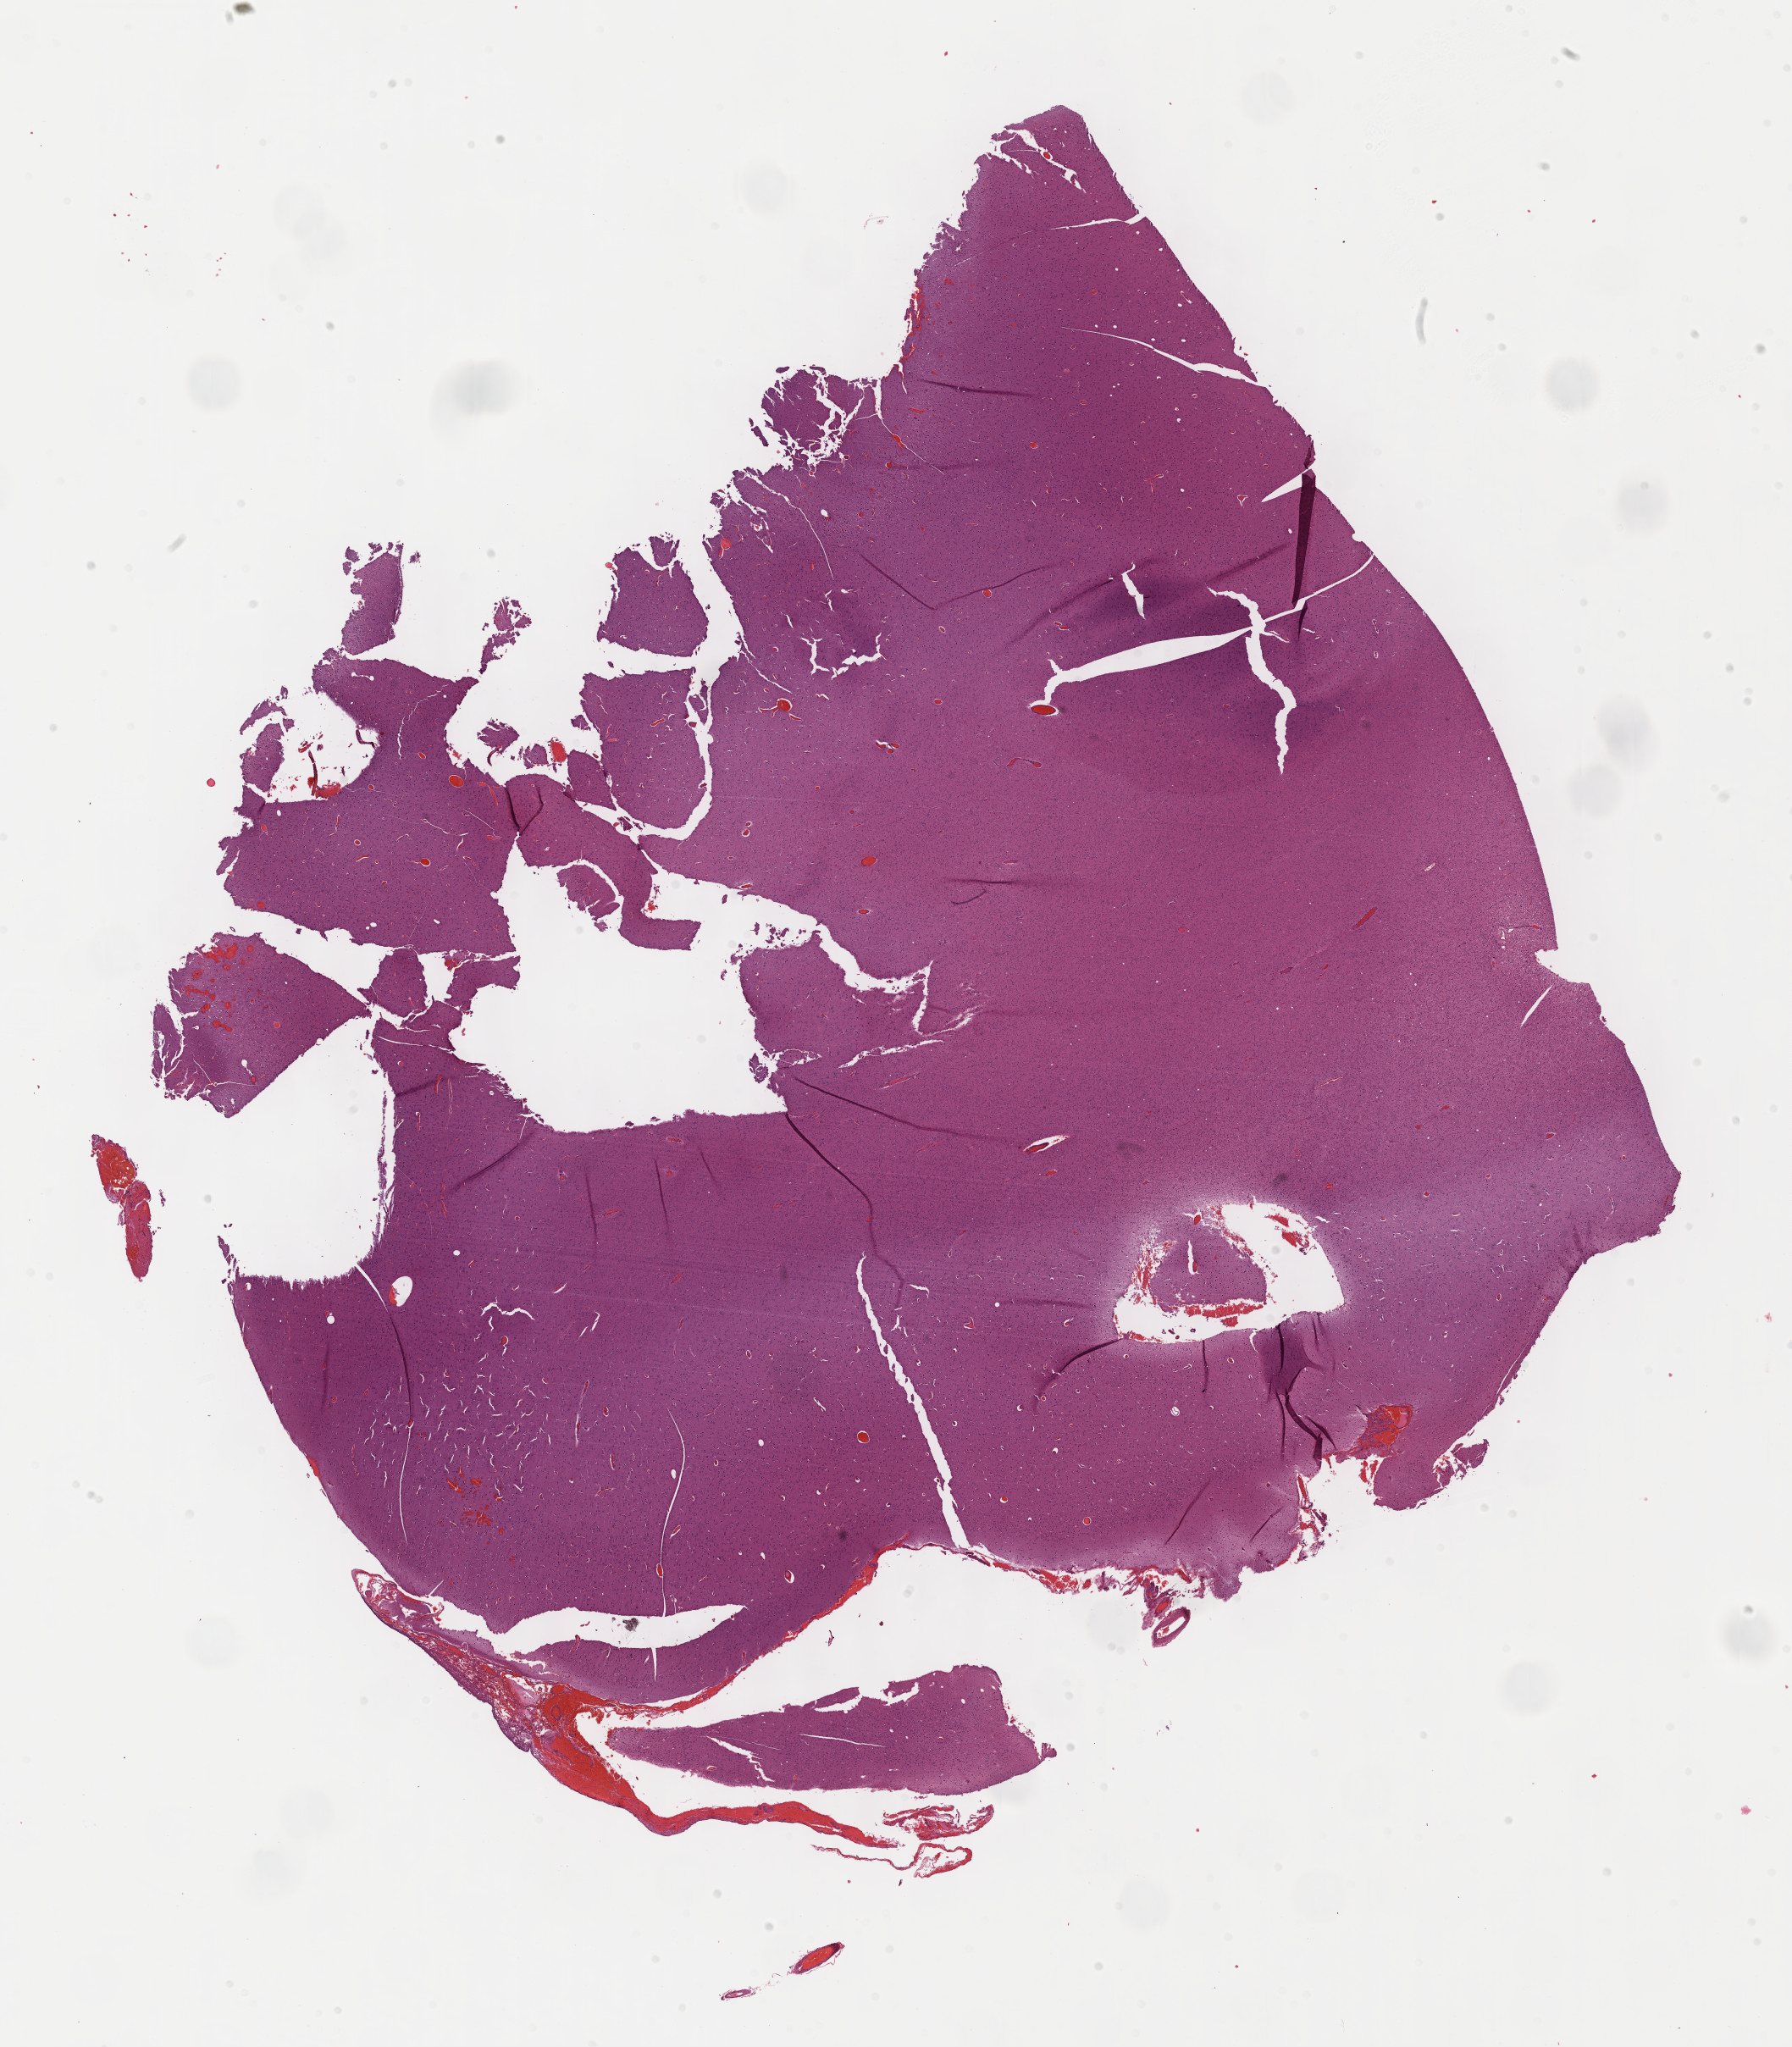
Digitized H&E tissue section (whole slide) — shown as a low-resolution overview of the whole scanned area (about 17.1 x 19.5 mm, slide scanned at 40x). Formalin-fixed paraffin-embedded (FFPE) diagnostic section. Brain, primary tumour sample. Male patient; age at initial diagnosis 33 years. Histologic grade: G2 (moderately differentiated).
Diagnosis: Oligodendroglioma, NOS. Laterality: right.